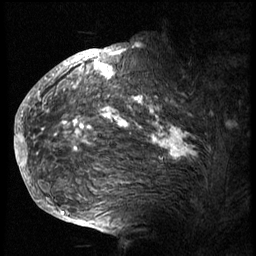
Breast MRI (dynamic contrast-enhanced), one sagittal slice; slice 50 of 74 in the series (ordered by position); 3 images stored at this slice position (order not interpretable as contrast timing); 1.5 T; TE 4.2 ms, TR 8.9 ms; 2.5 mm slice thickness; 256 × 256 image matrix, field of view 200 × 200 mm. Patient: female, 57 years. From the clinical record (not read from this slice): setting: breast cancer imaged before/during neoadjuvant chemotherapy; receptor status: HER2-positive.
Annotated regions visible in this slice (semi-automatic segmentation, software-assisted and operator-edited):
- analysis volume of interest (the breast-tissue region the enhancement analysis was run in; not a lesion): bounding box [x1, y1, x2, y2] px = [40, 62, 239, 175]
- tumour enhancement mask (voxels above the 140 % enhancement threshold inside the analysis volume of interest): [40, 62, 193, 160]